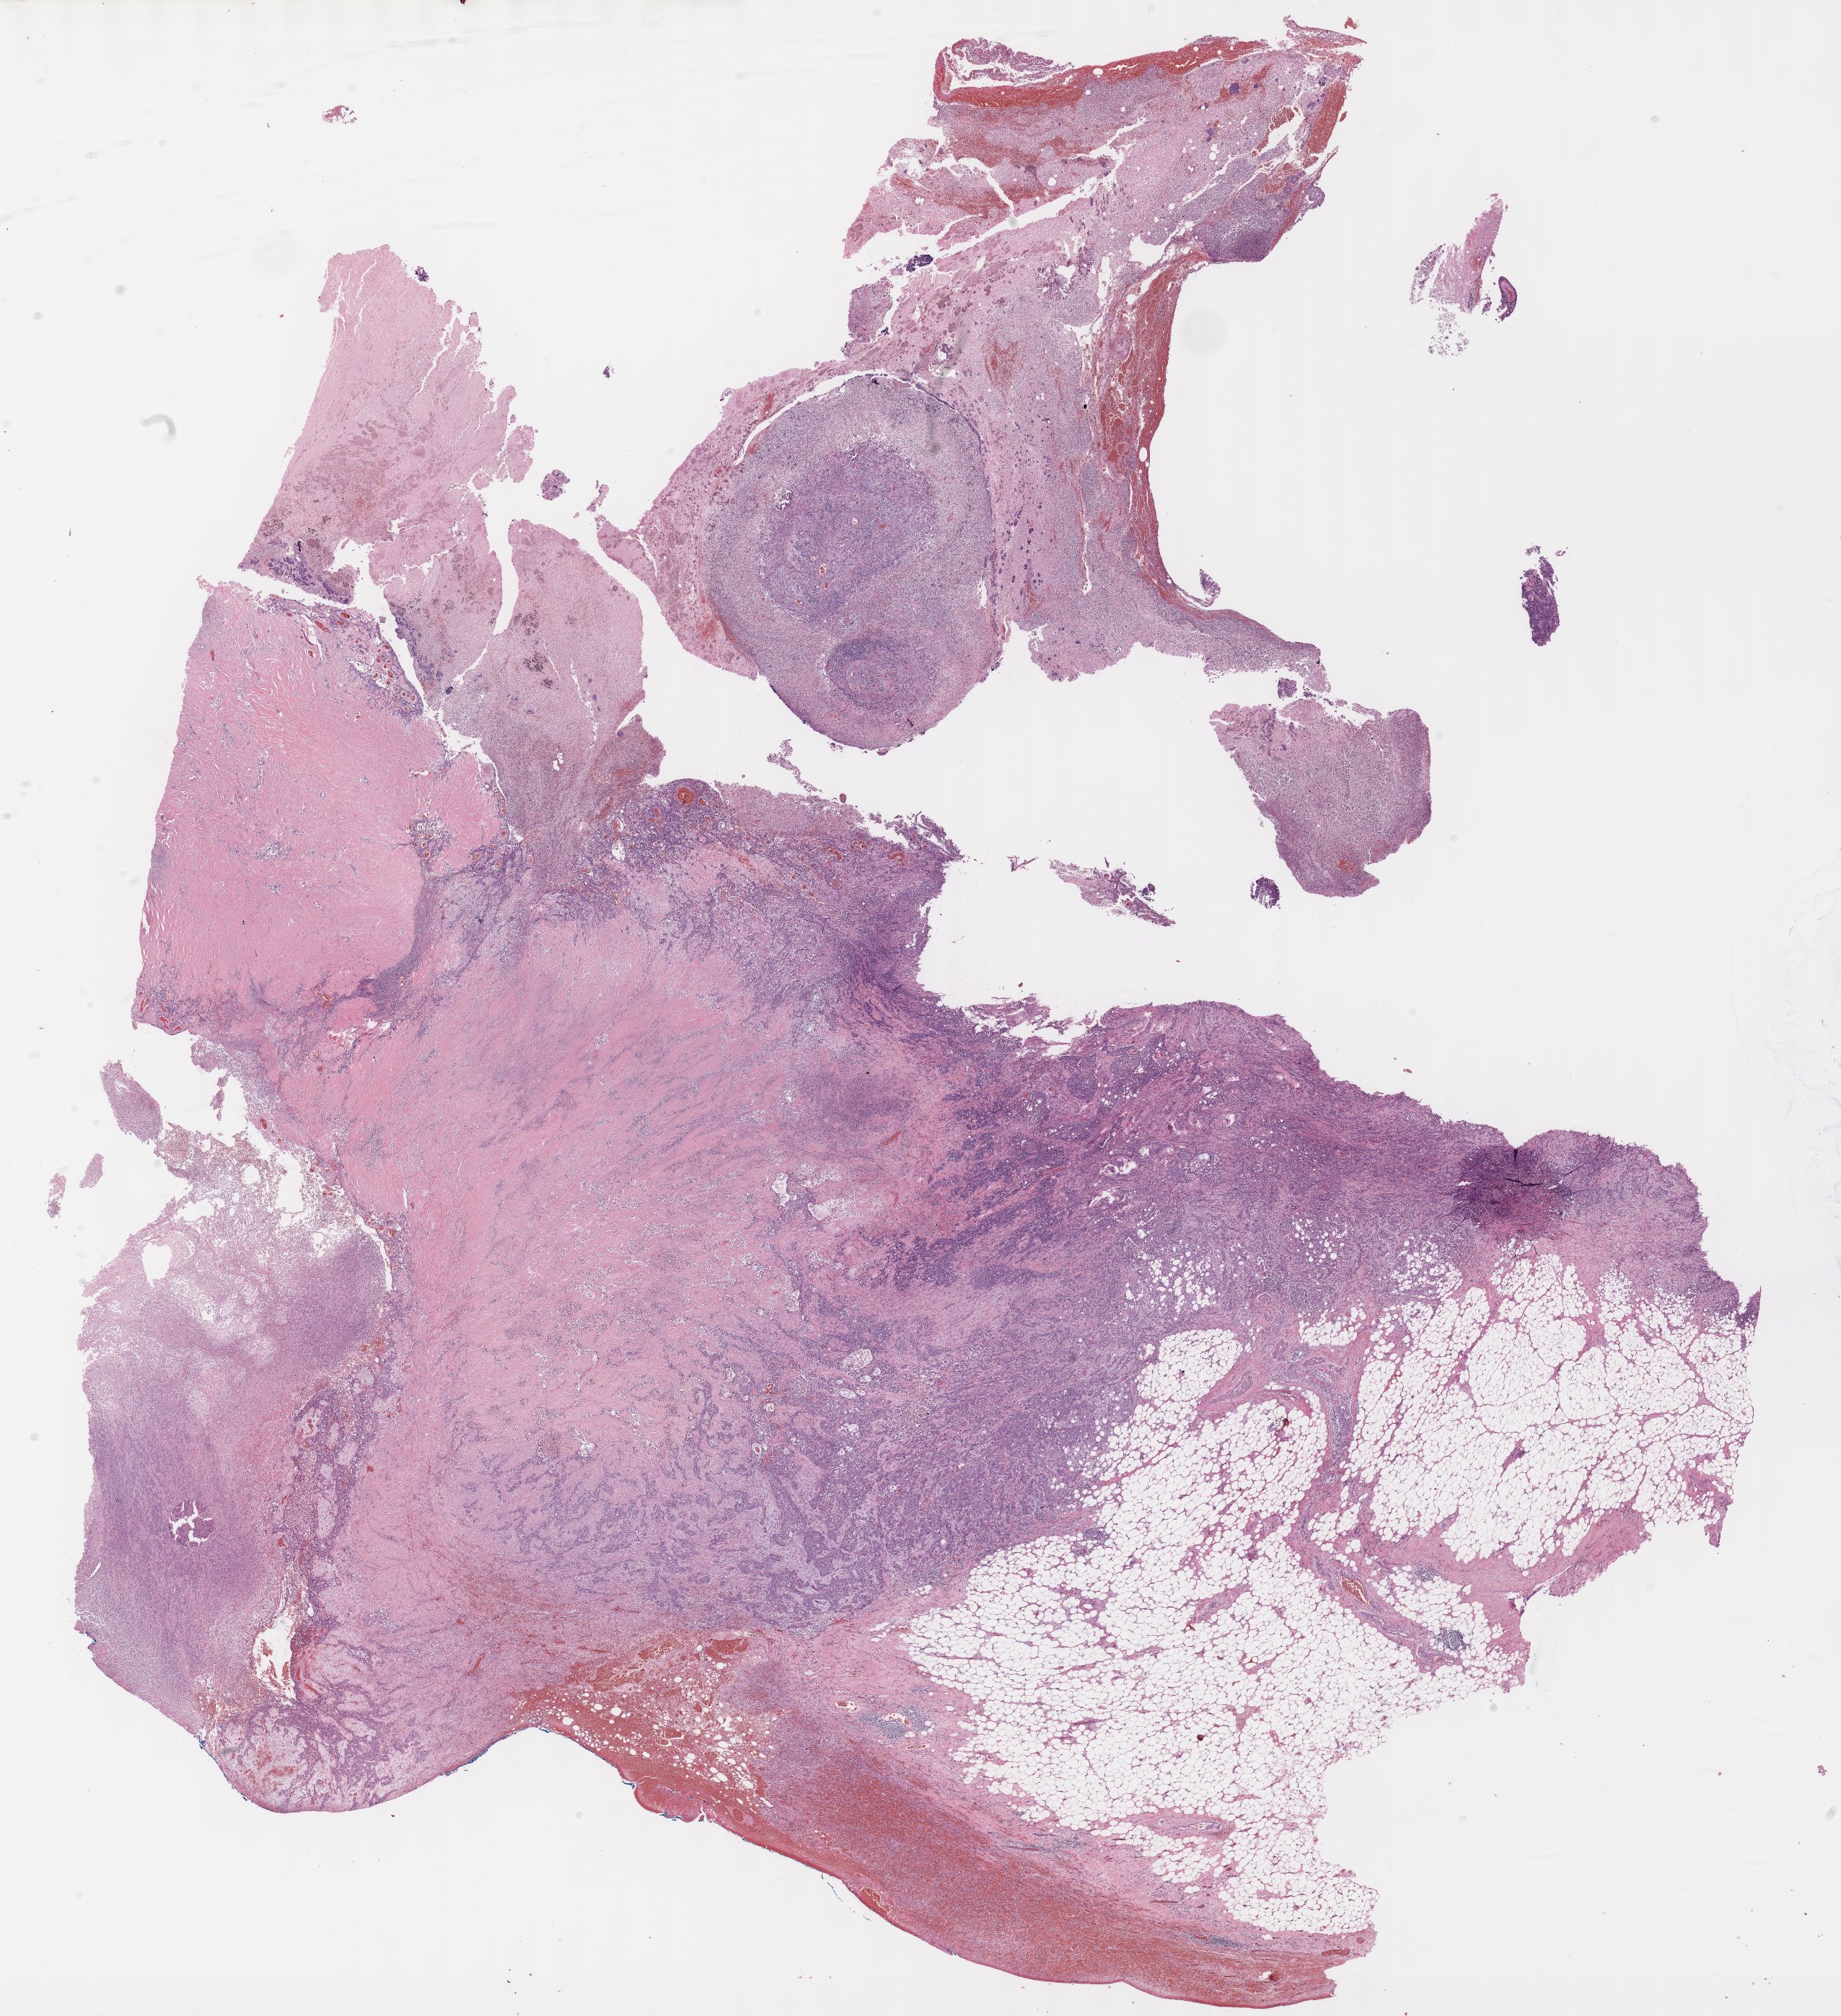
Whole-slide histology image, H&E-stained — a low-resolution overview of the entire scanned area, about 20.6 x 22.6 mm, FFPE section, sample: primary tumour, bladder. Patient: male, age at initial diagnosis 66 years.
Diagnosis: Transitional cell carcinoma.